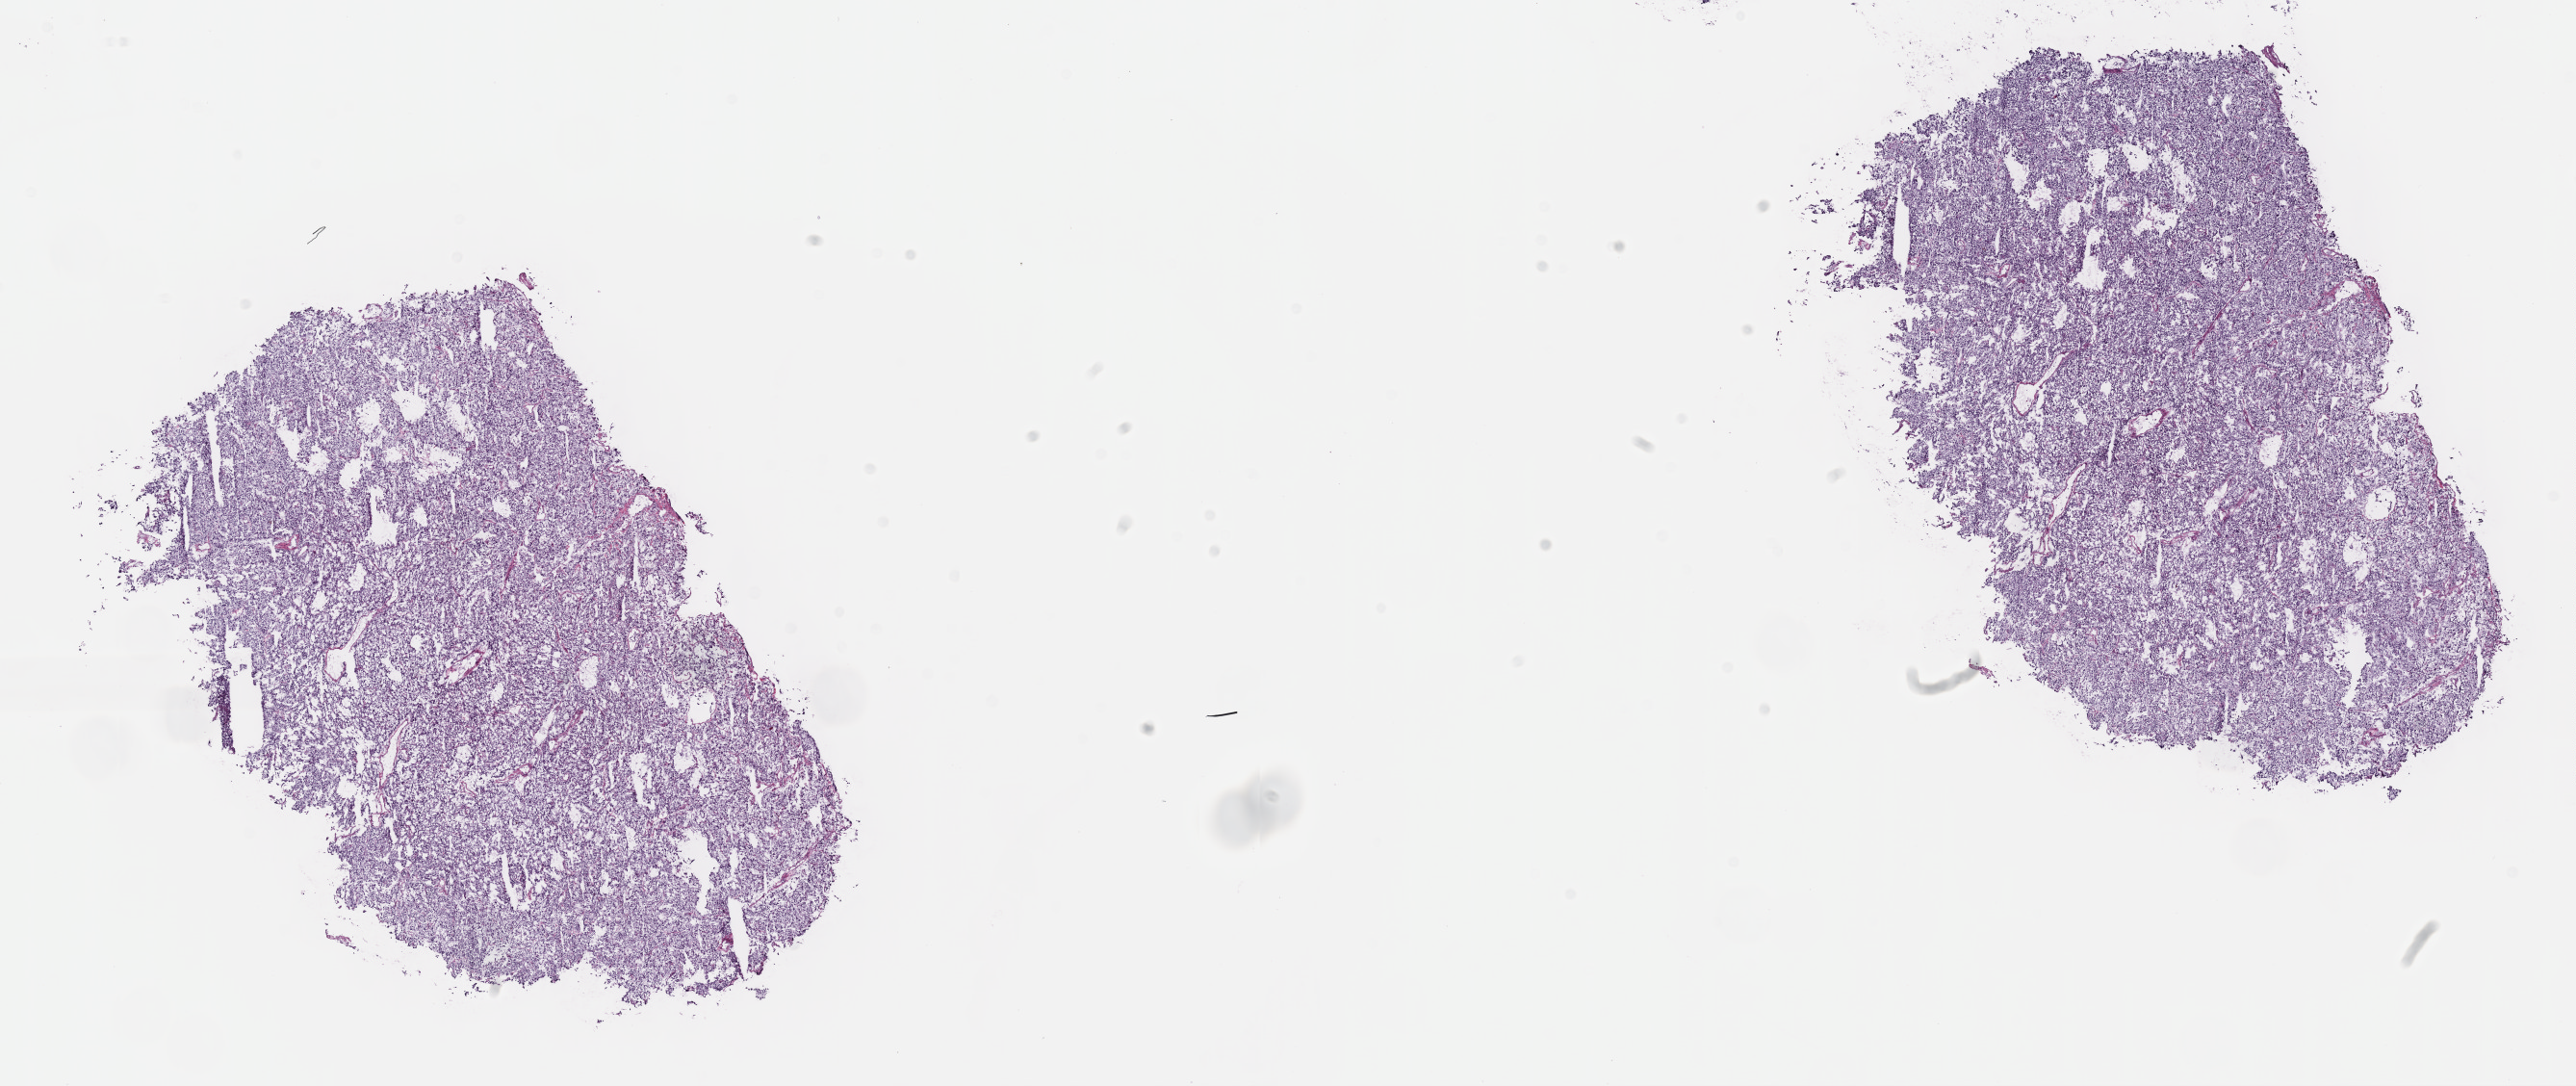
Digitized H&E tissue section (whole slide) — whole scanned area (about 21.6 x 9.1 mm, acquisition: 40x scan) shown as a low-resolution overview, frozen section from the top of the tissue portion, primary tumour sample from the adrenal gland. Patient: female, age at initial diagnosis 42 years. Composition of this section per pathologist review: tumour cells 90%, tumour nuclei 95%, normal cells 0%, stromal cells 10%, necrosis 0%. Inflammatory infiltration, as recorded: lymphocyte infiltration 0%, monocyte infiltration 0%, neutrophil infiltration 0%.
Pathologic diagnosis: Pheochromocytoma, NOS.